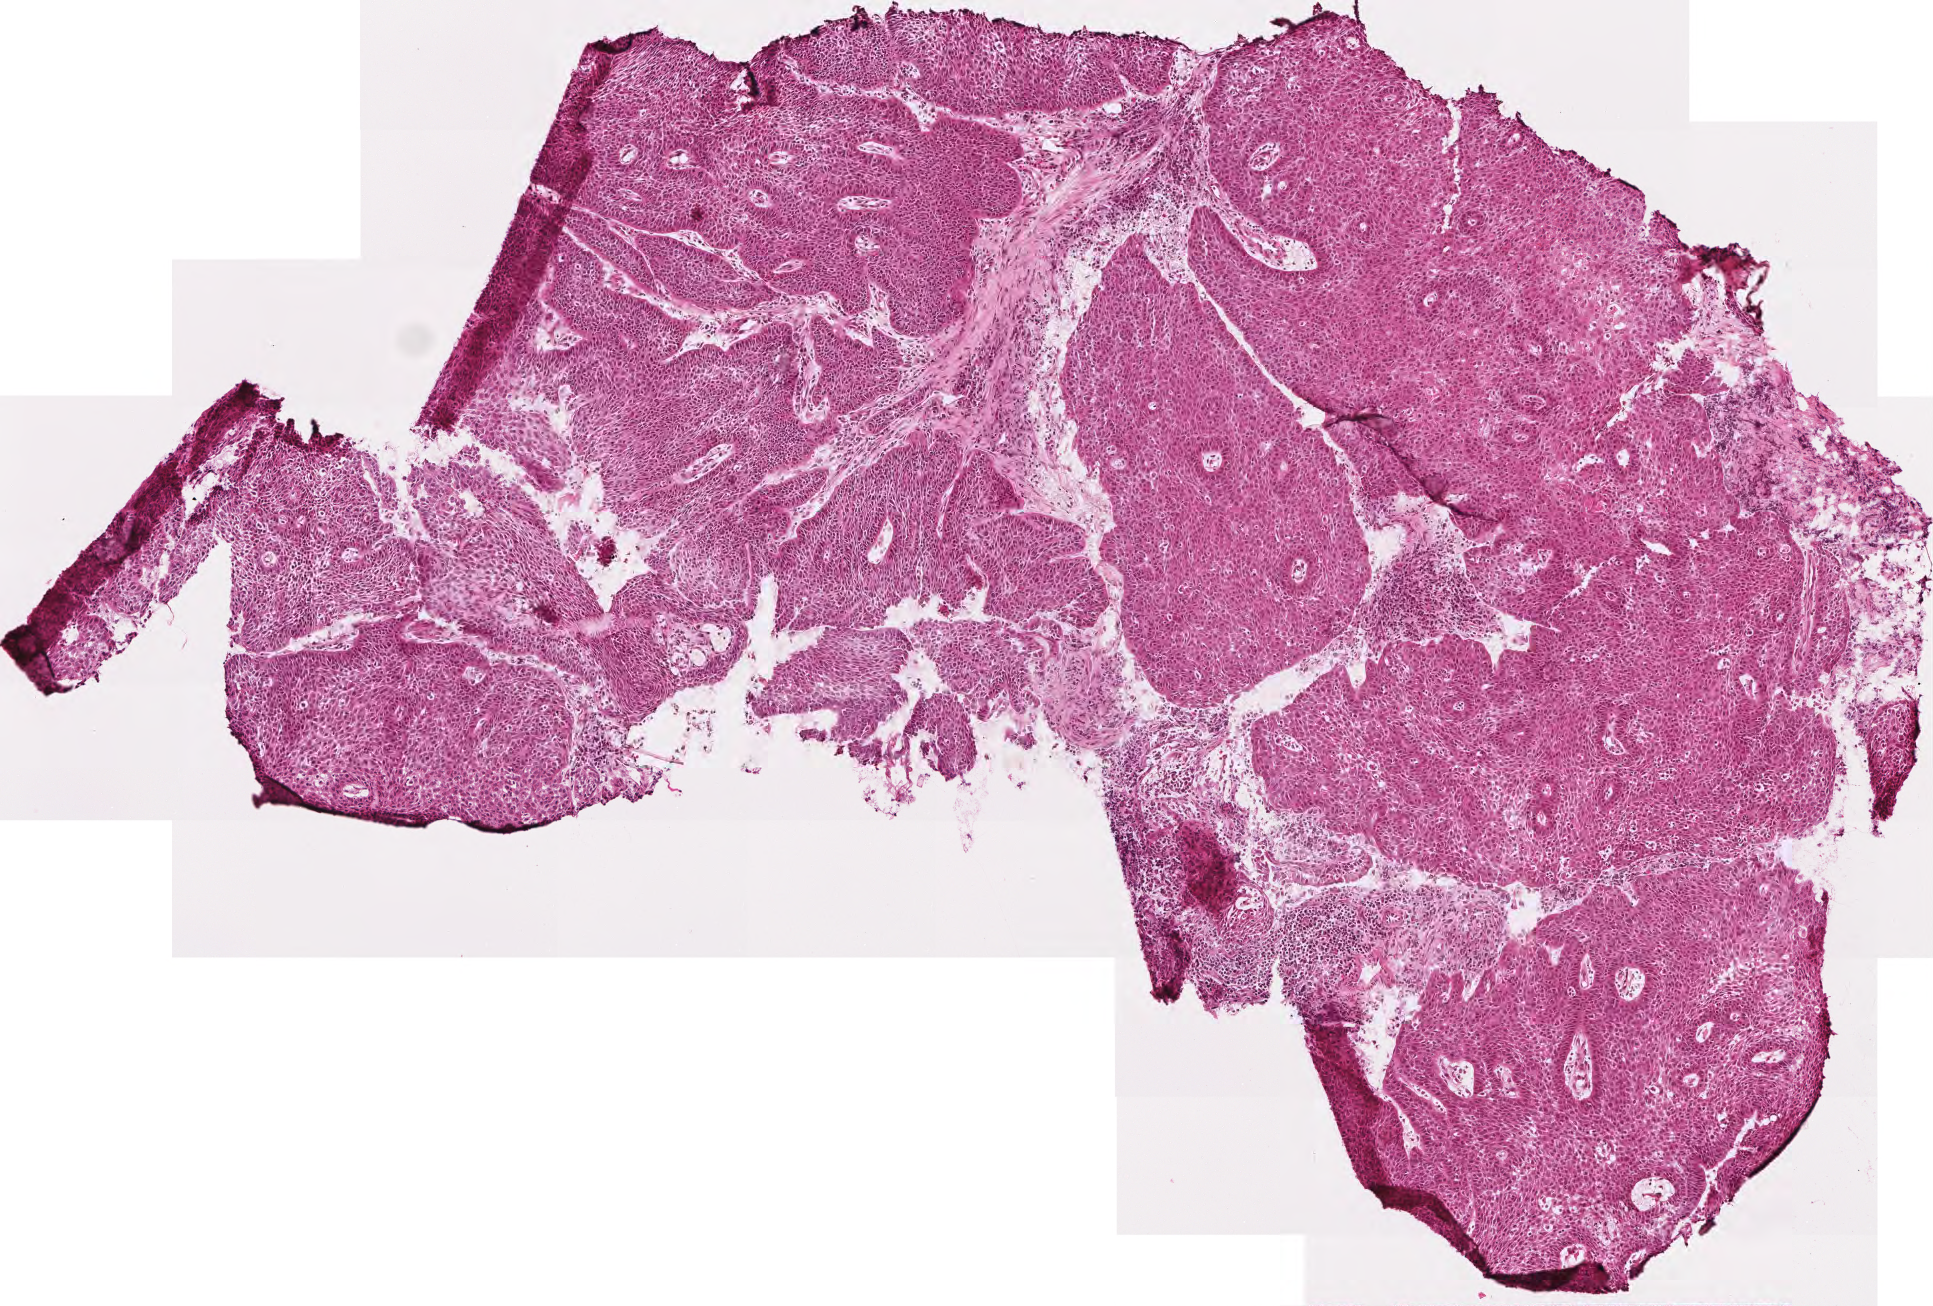
H&E-stained whole-slide image, shown as a low-resolution overview of the whole scanned area (about 3.9 x 2.6 mm). Frozen section from the top of the tissue portion. Head and neck, primary tumour sample. Male, age 68 years at initial diagnosis. Histologic grade: G2 (moderately differentiated). Pathologist review of this section (percent, as recorded): tumour cells 95%, tumour nuclei 85%, normal cells 0%, stromal cells 5%, necrosis 0%. Infiltration values recorded for this section: lymphocyte infiltration 8%.
Pathologic diagnosis: Squamous cell carcinoma, NOS (larynx, NOS).